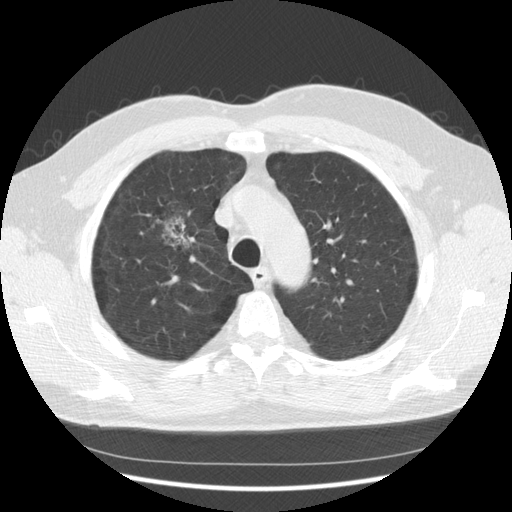
Low-dose screening chest CT, axial slice. Third screening round (two years after baseline). Lung window (W 1500 / L -600 HU). 2.5 mm slice thickness. 140 kVp. Slice 95 of 133 in the series. 512 × 512 image matrix. Male, age 60 years at enrolment.
Lesion marked by an expert reader, box from (x=141, y=200) to (x=202, y=268) px. The exam's reader record, not a measurement of the box and not confirmed to be the same lesion: non-calcified nodule or mass ≥4 mm, right upper lobe, poorly defined margins, mixed attenuation, pre-existing on the prior screen: yes; interval growth: yes. Official screen result: positive, other.